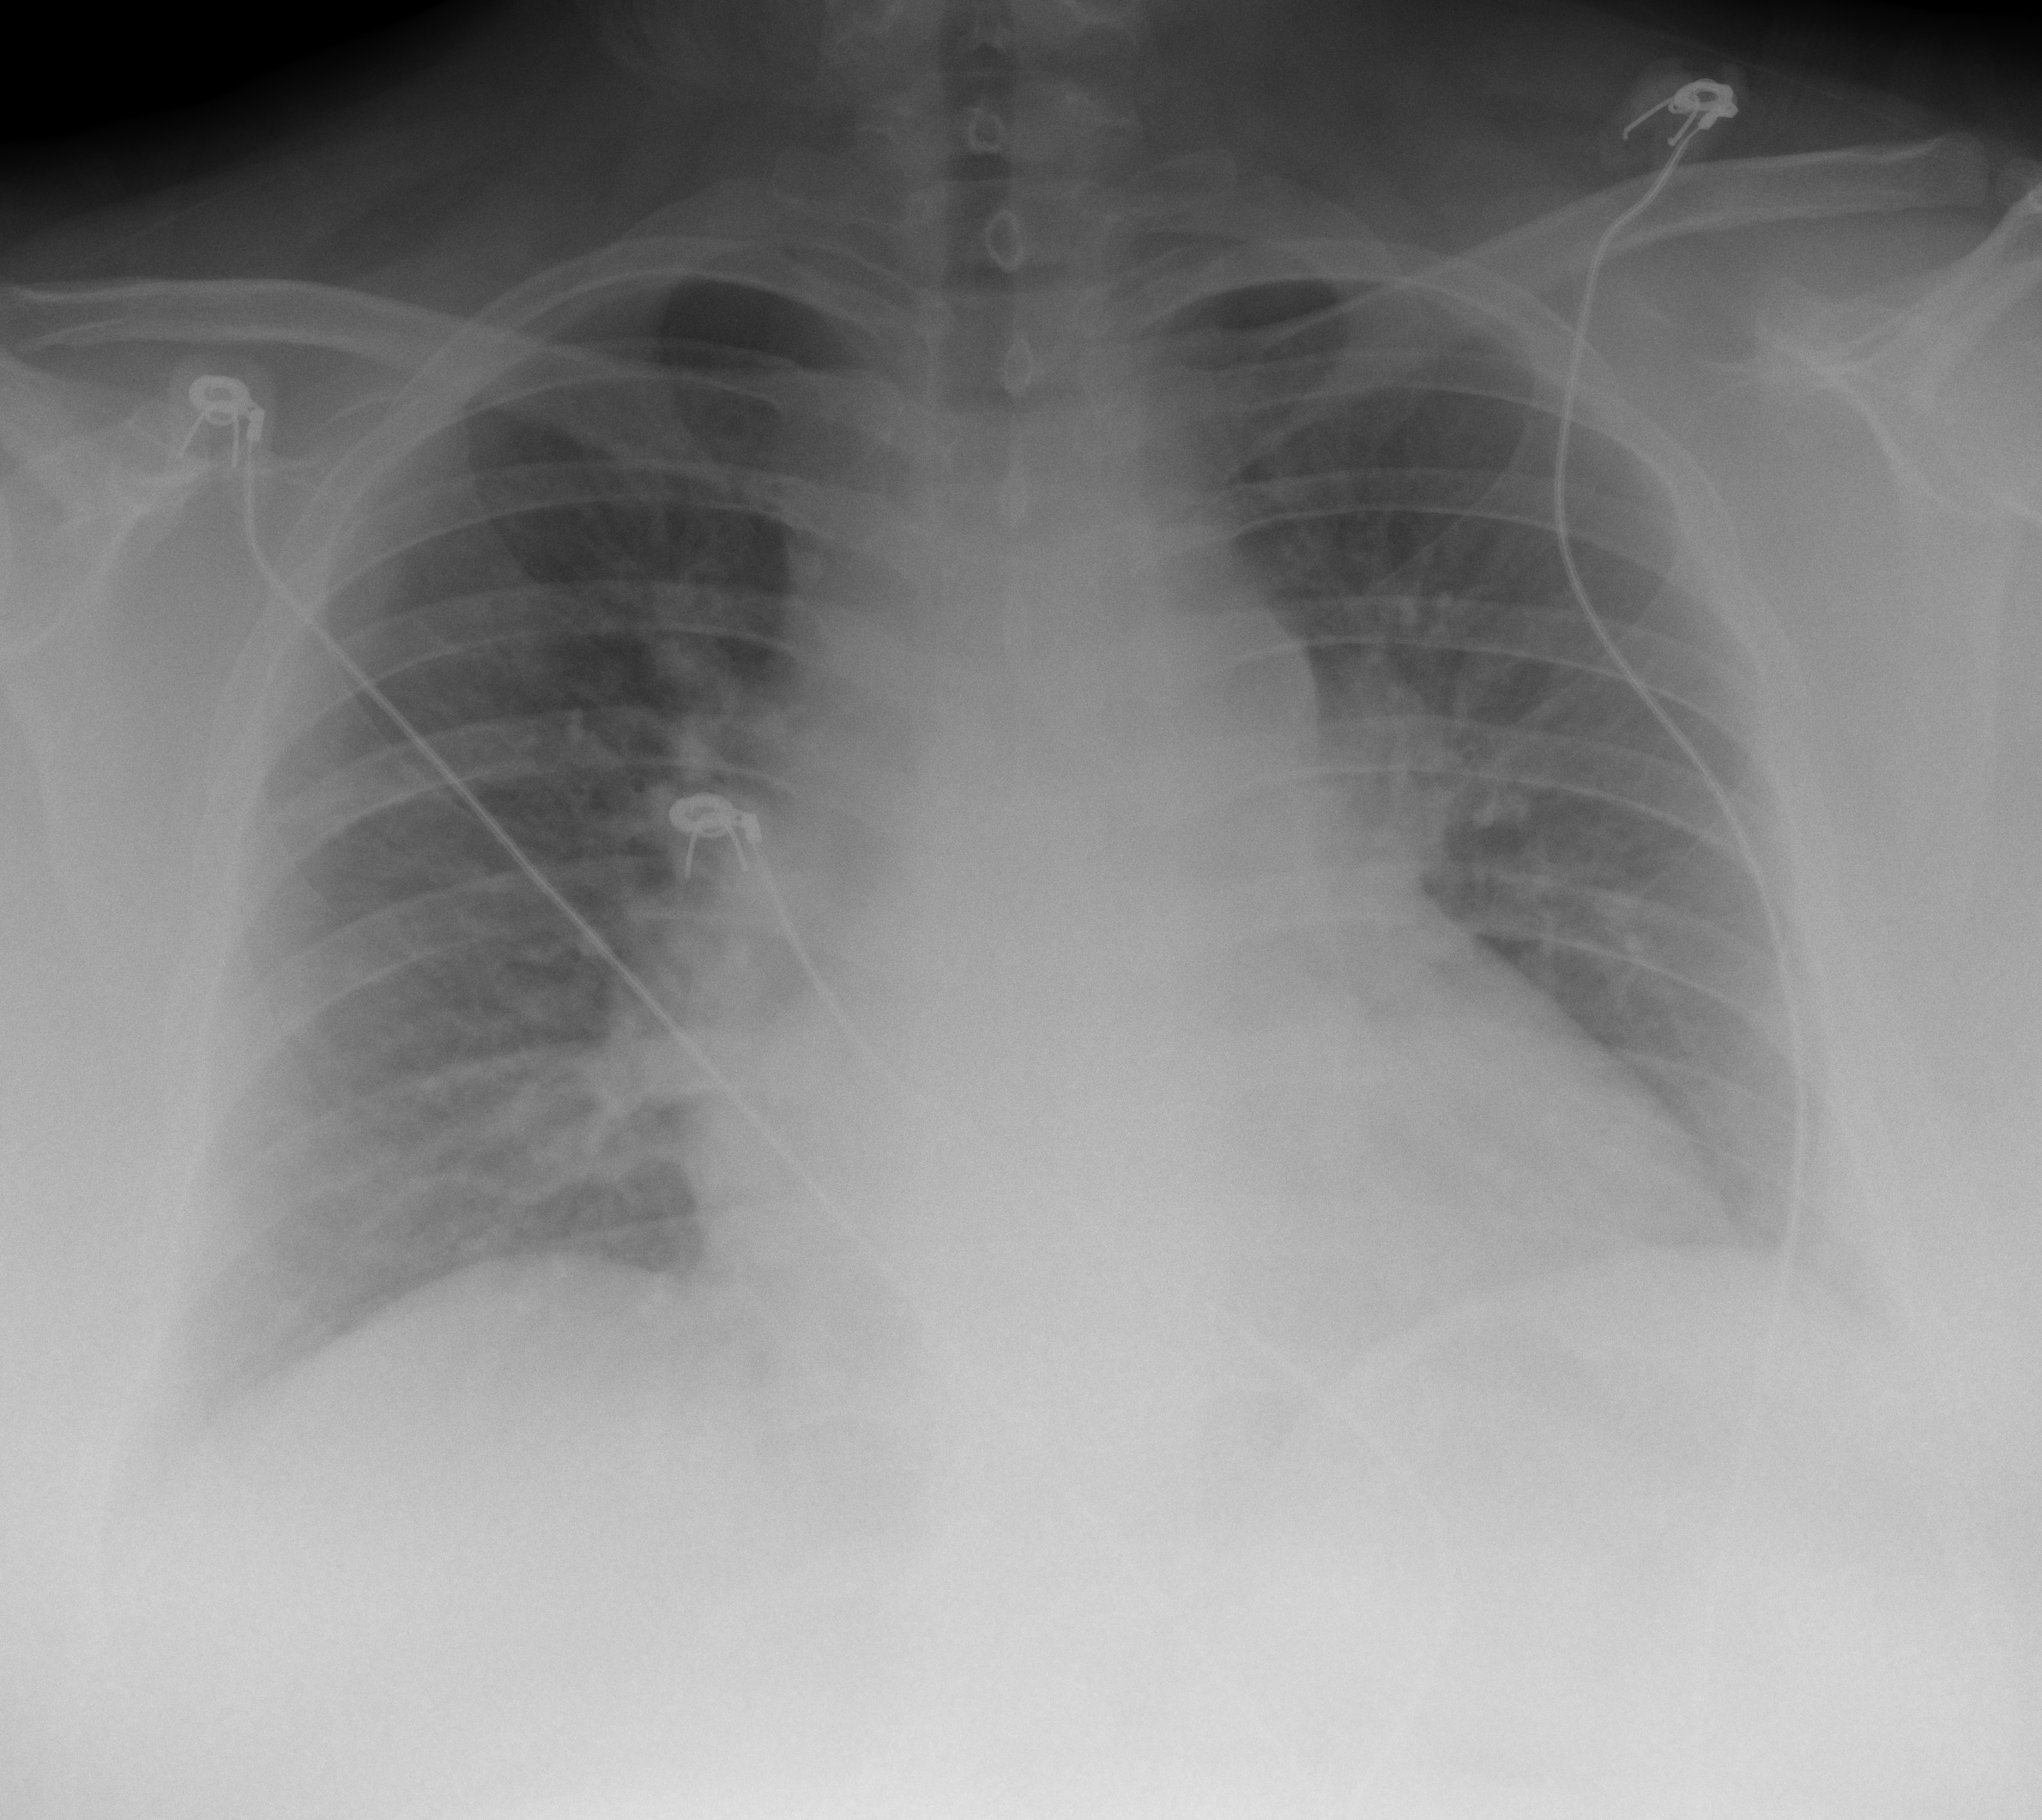
Chest X-ray (portable), AP projection. Female patient, age 29 years; imaged 0 days after the COVID-19 diagnosis.
Radiologist key findings (as recorded): No dense consolidation or pleural effusion.